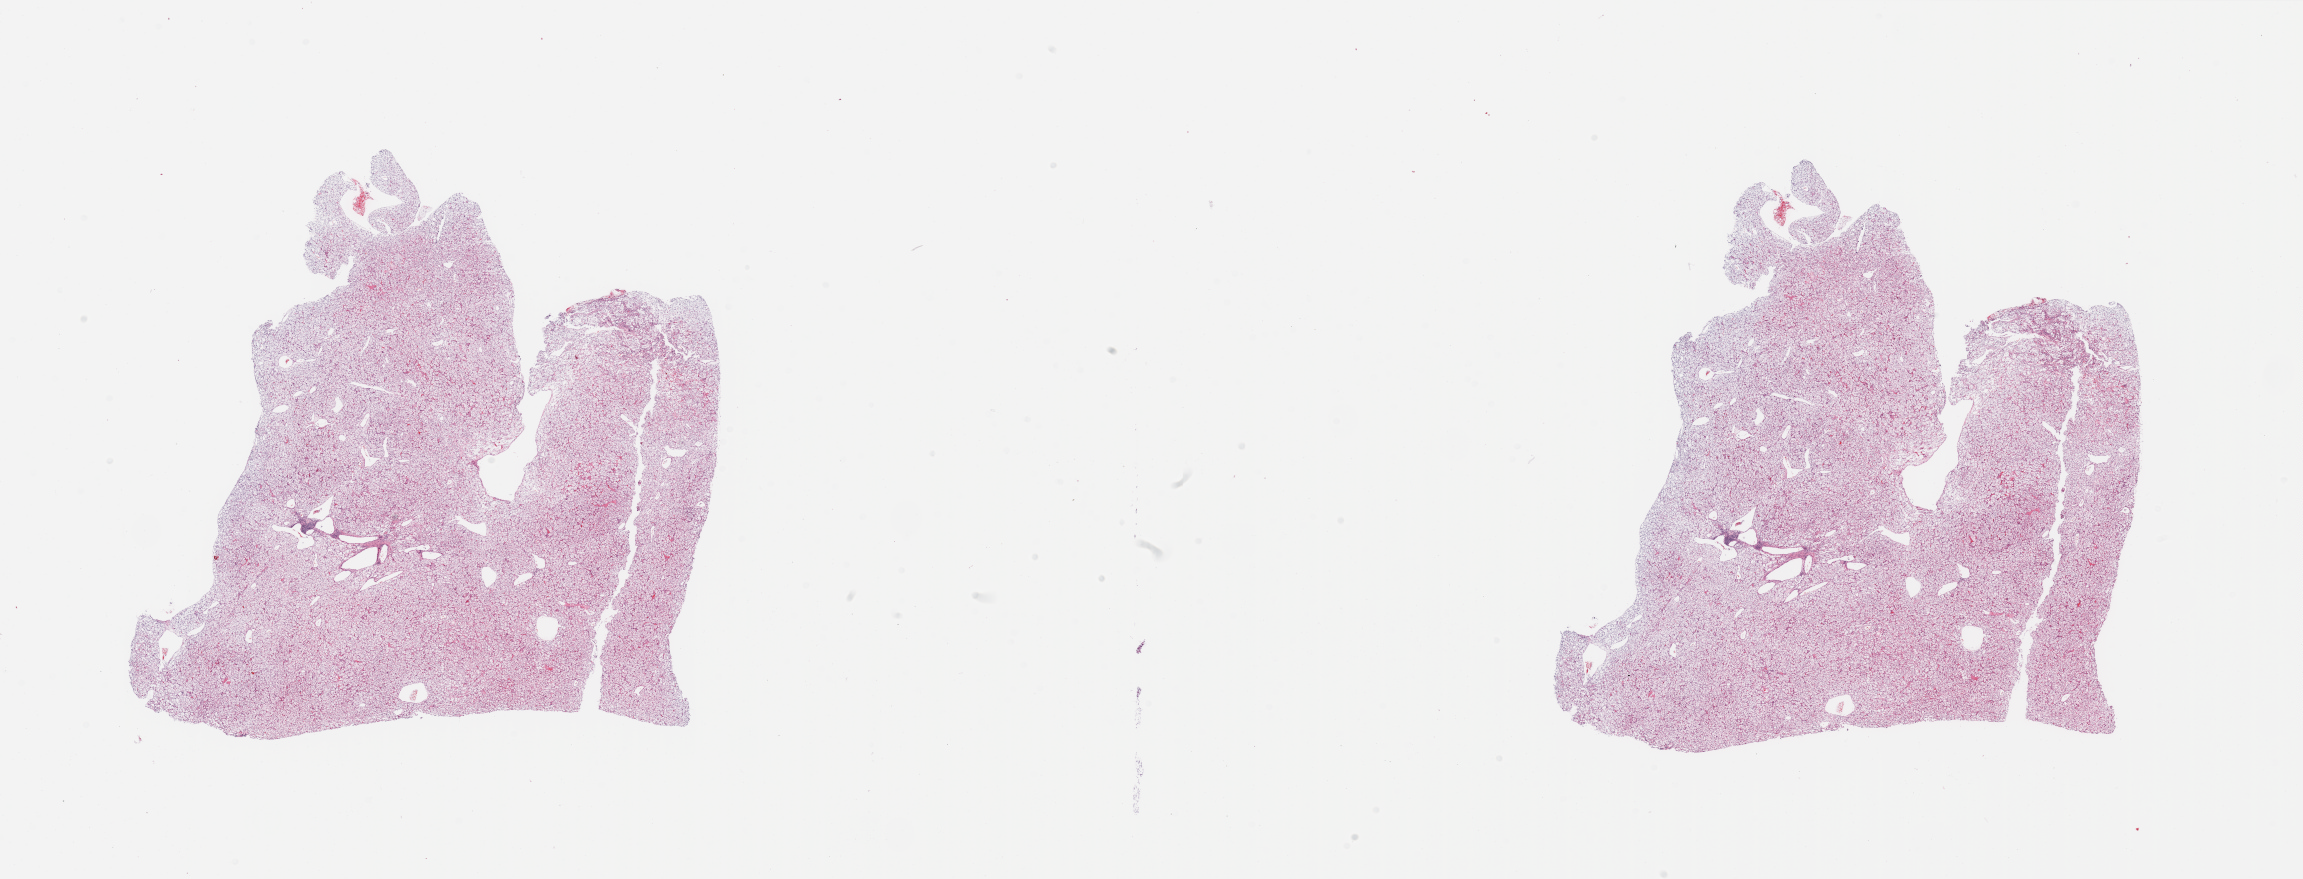
Whole-slide histology image, H&E-stained — a low-resolution overview of the entire scanned area, about 36.4 x 13.9 mm (slide scanned at 20x); kidney, tumour tissue. Female, 72 y/o. Histologic grade: G4 (undifferentiated).
Diagnosis: Renal cell carcinoma, NOS. AJCC pathologic stage: III. Primary tumour site (as recorded): middle.